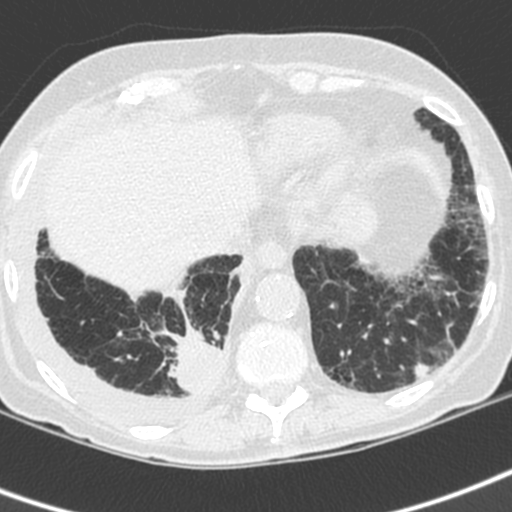
Low-dose screening chest CT, axial slice; first (baseline) screen; lung window (W 1500 / L -600 HU); 1.3 mm slice thickness; slice 153 of 192 in the series; 512 × 512 image matrix, field of view 288 × 288 mm. Female participant, aged 73 years at enrolment. Current smoker at enrolment.
• Expert-annotated lung lesion, bounding box [x1, y1, x2, y2] px = [160, 325, 235, 405].
• Screening reader's record for this exam (one nodule recorded; not confirmed to be the boxed lesion): non-calcified nodule or mass ≥4 mm, right lower lobe, 35 × 30 mm, spiculated (stellate) margins, soft tissue attenuation.
• Later outcome: lung cancer diagnosed 22 days after this screen — adenocarcinoma, NOS, right lower lobe, stage IV (AJCC 6th edition), 35 mm at pathology.